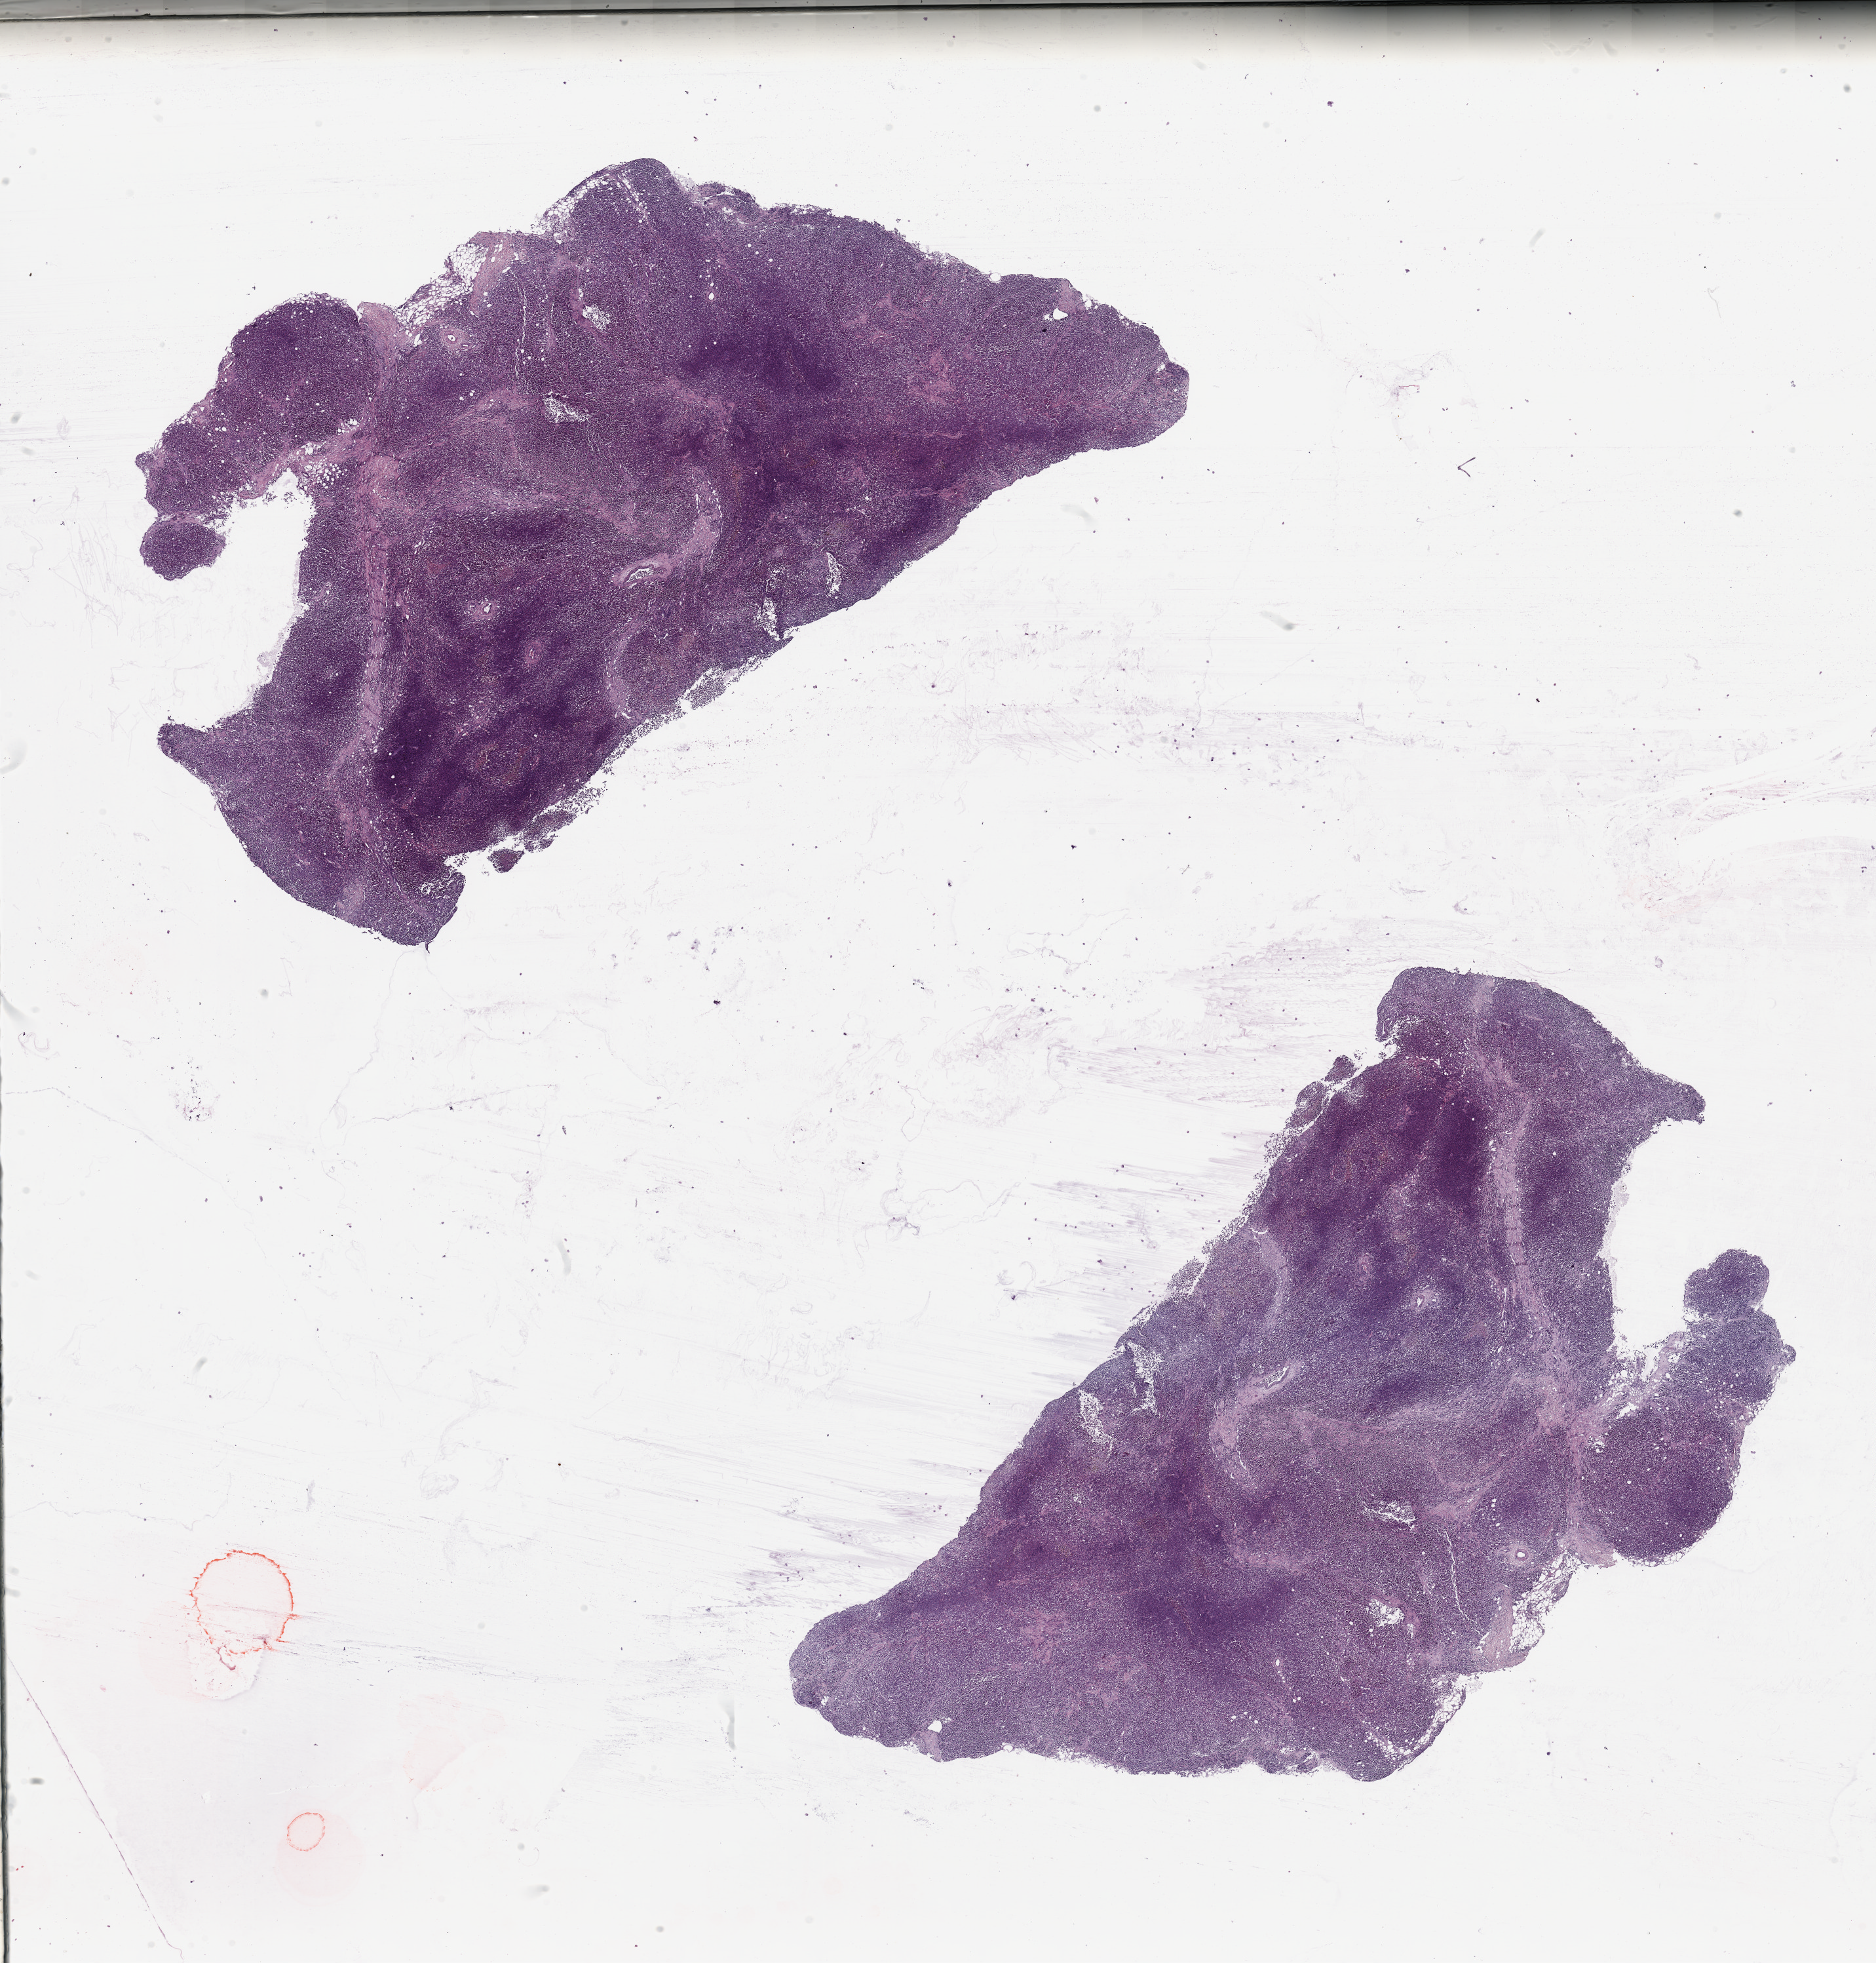
Digitized Hematoxylin and eosin (H&E) stained tissue section (whole slide) — a low-resolution overview of the entire scanned area, about 22.6 x 23.7 mm (slide scanned at 20x). Melanoma tumour tissue; sampled site not recorded. Patient: male, age 45 years.
AJCC pathologic stage: IIB. Primary tumour site (as recorded): trunk. Histologic diagnosis: Malignant melanoma, NOS.